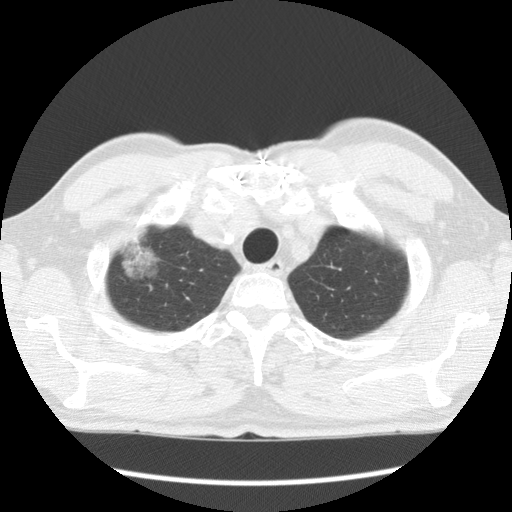
Axial slice from a low-dose chest CT screening exam; baseline screening round; lung window (W 1500 / L -600 HU); 512 × 512 image matrix, field of view 340 × 340 mm. Male participant, aged 64 years at enrolment. Former smoker at enrolment.
Lesion marked by an expert reader, box from (x=108, y=218) to (x=170, y=282) px. The screening reader recorded 2 non-calcified nodules or masses ≥4 mm on this exam (right upper lobe, left upper lobe); which of them this box marks is not recorded.